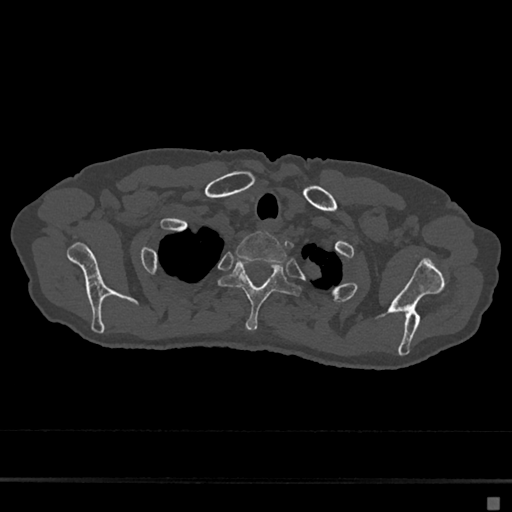
CT including the spine, one axial slice. Position 583 of 797 along the scan axis. Reconstruction kernel Br40s/3. Bone window (W 1800 / L 400 HU). 0.5 mm slice thickness. 512 × 512 image matrix, field of view 360 × 360 mm. Female patient, age 68 years. From the clinical record (not read from this slice): primary cancer: renal.
Outlined on this slice (semi-automatically segmented with operator editing):
- T1 vertebra: bounding box (x1, y1, x2, y2) in pixels: (236, 231, 286, 263)
- T2 vertebra: (219, 256, 300, 331)